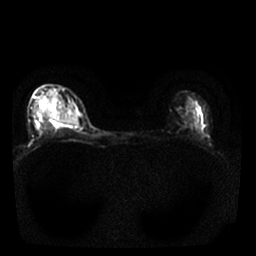
Breast MRI, one axial slice. Position 17 of 25 along the scan axis. Diffusion-weighted series; image 2 of 4 stored at this slice position (different b-values; order by instance number). 1.5 T. 4 mm slice thickness. 256 × 256 image matrix, field of view 310 × 310 mm. Female patient.
Outlined on this slice (manually delineated by an expert):
- tumour on diffusion-weighted imaging: bounding box <40,108,79,125> (left, top, right, bottom; pixels)